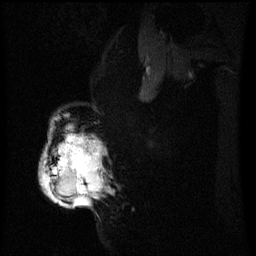
Breast MRI (dynamic contrast-enhanced), one sagittal slice; slice 42 of 60 in the series (ordered by position); dynamic contrast-enhanced series, image 2 of 3 at this slice position (ordered by acquisition); 1.5 T; TE 4.2 ms, TR 8 ms; 2.2 mm slice thickness; 256 × 256 image matrix, field of view 200 × 200 mm. Female patient, age 50 years.
Outlined on this slice (semi-automatic segmentation, software-assisted and operator-edited):
- analysis volume of interest (the breast-tissue region the enhancement analysis was run in; not a lesion): bounding box [x1, y1, x2, y2] px = [41, 122, 104, 207]
- tumour enhancement mask (voxels above the 70 % enhancement threshold inside the analysis volume of interest): [43, 136, 100, 207]